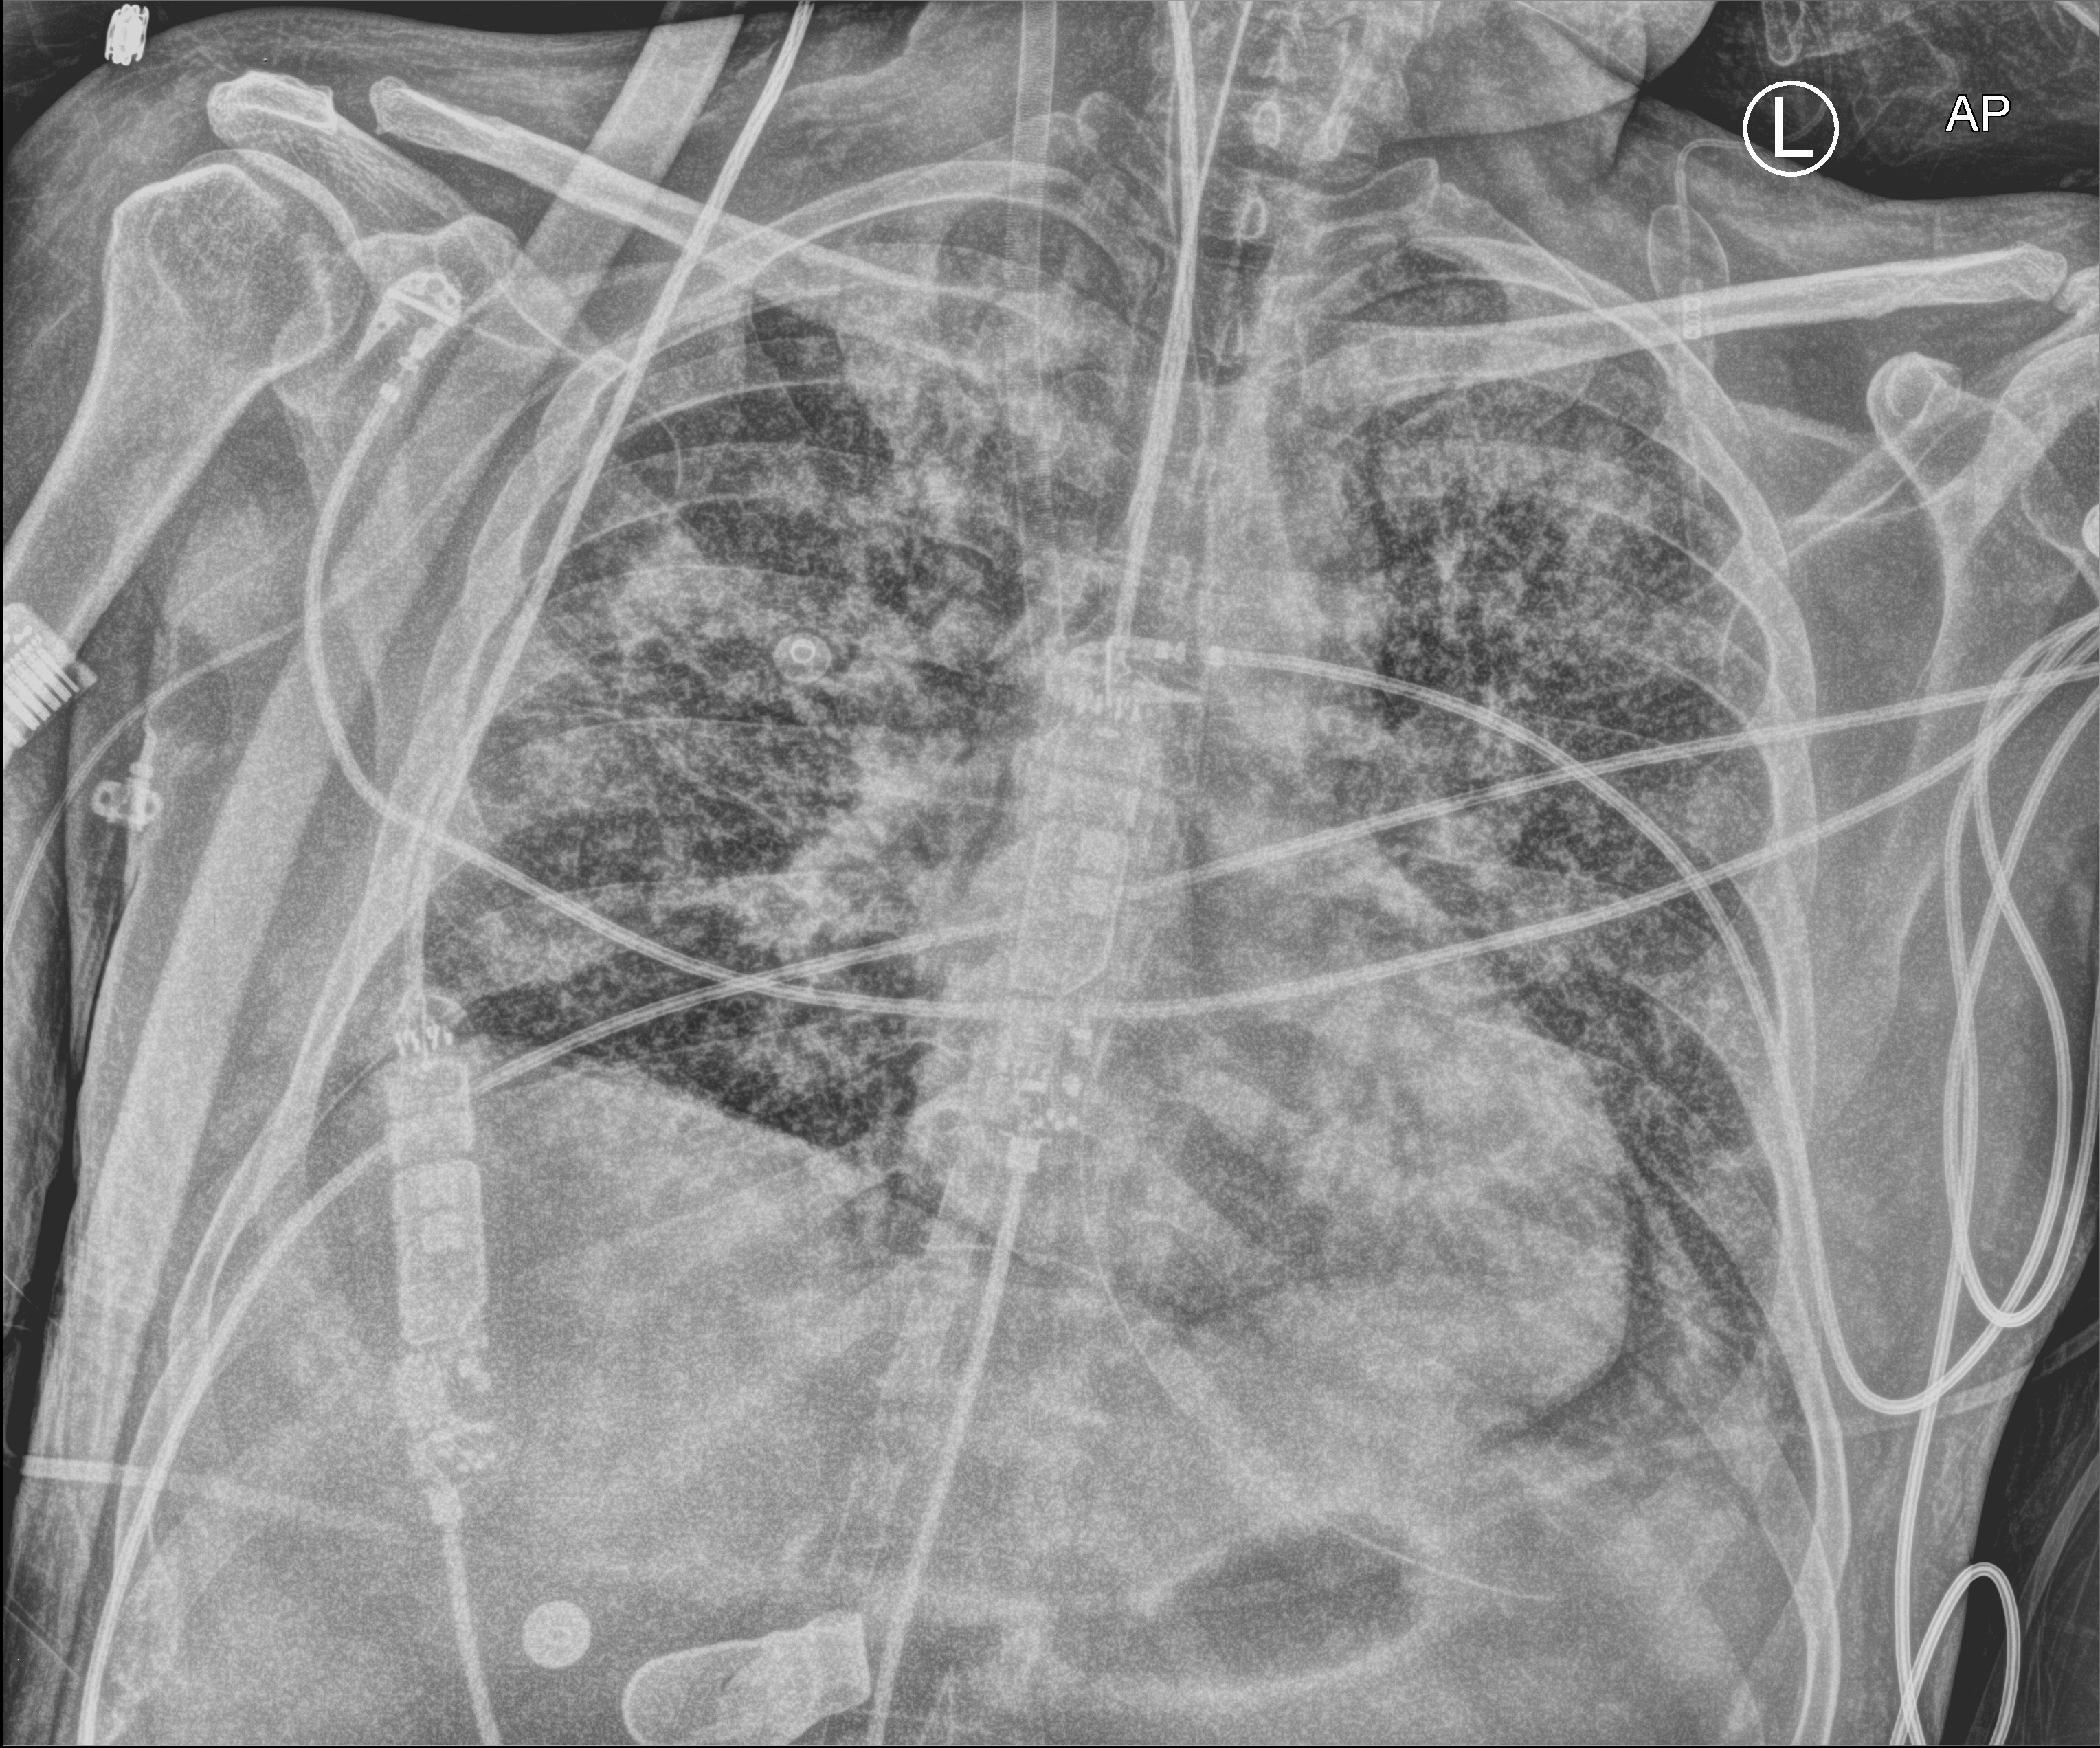
Portable chest radiograph, anteroposterior (AP) projection. Patient hospitalised with COVID-19; male, aged 18–59 years.
Hospital-stay facts (about this admission, not read from this image; timing relative to this image not recorded): other chronic lung disease (admission record): no; mechanically ventilated during this hospital stay: yes.